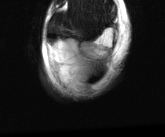
MRI of an extremity soft-tissue mass, one axial slice. Position 11 of 81 along the scan axis. T2-weighted fat-saturated. MR volume resampled by the dataset authors to the PET/CT grid (not the native acquisition matrix). 3.27 mm slice thickness. 165 × 137 image matrix. Male patient. Case-level facts recorded for this patient, not image findings: histological type: liposarcoma - round cell; grade: high; site of the primary tumour: right calf.
Annotated regions visible in this slice (expert contour drawn on MRI and transferred to this co-registered scan by the dataset authors):
- gross tumour volume (mass): bounding box <48,39,99,95> (left, top, right, bottom; pixels)